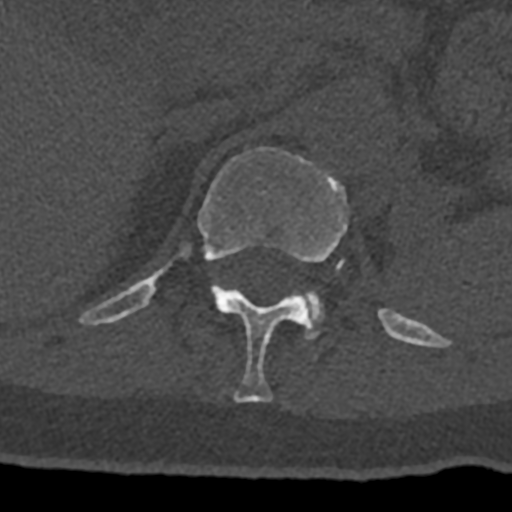
CT including the spine, one axial slice. Position 483 of 797 along the scan axis. Reconstruction kernel Br40s/3. 120 kVp. Bone window (W 1800 / L 400 HU). 0.5 mm slice thickness. 512 × 512 image matrix. Patient: male, 74 years. Case-level facts recorded for this patient, not image findings: primary cancer: renal.
Structures marked on this image (semi-automatic segmentation, software-assisted and operator-edited):
- L1 vertebra: bounding box <303,291,323,339> (left, top, right, bottom; pixels)
- T12 vertebra: <79,147,432,403>